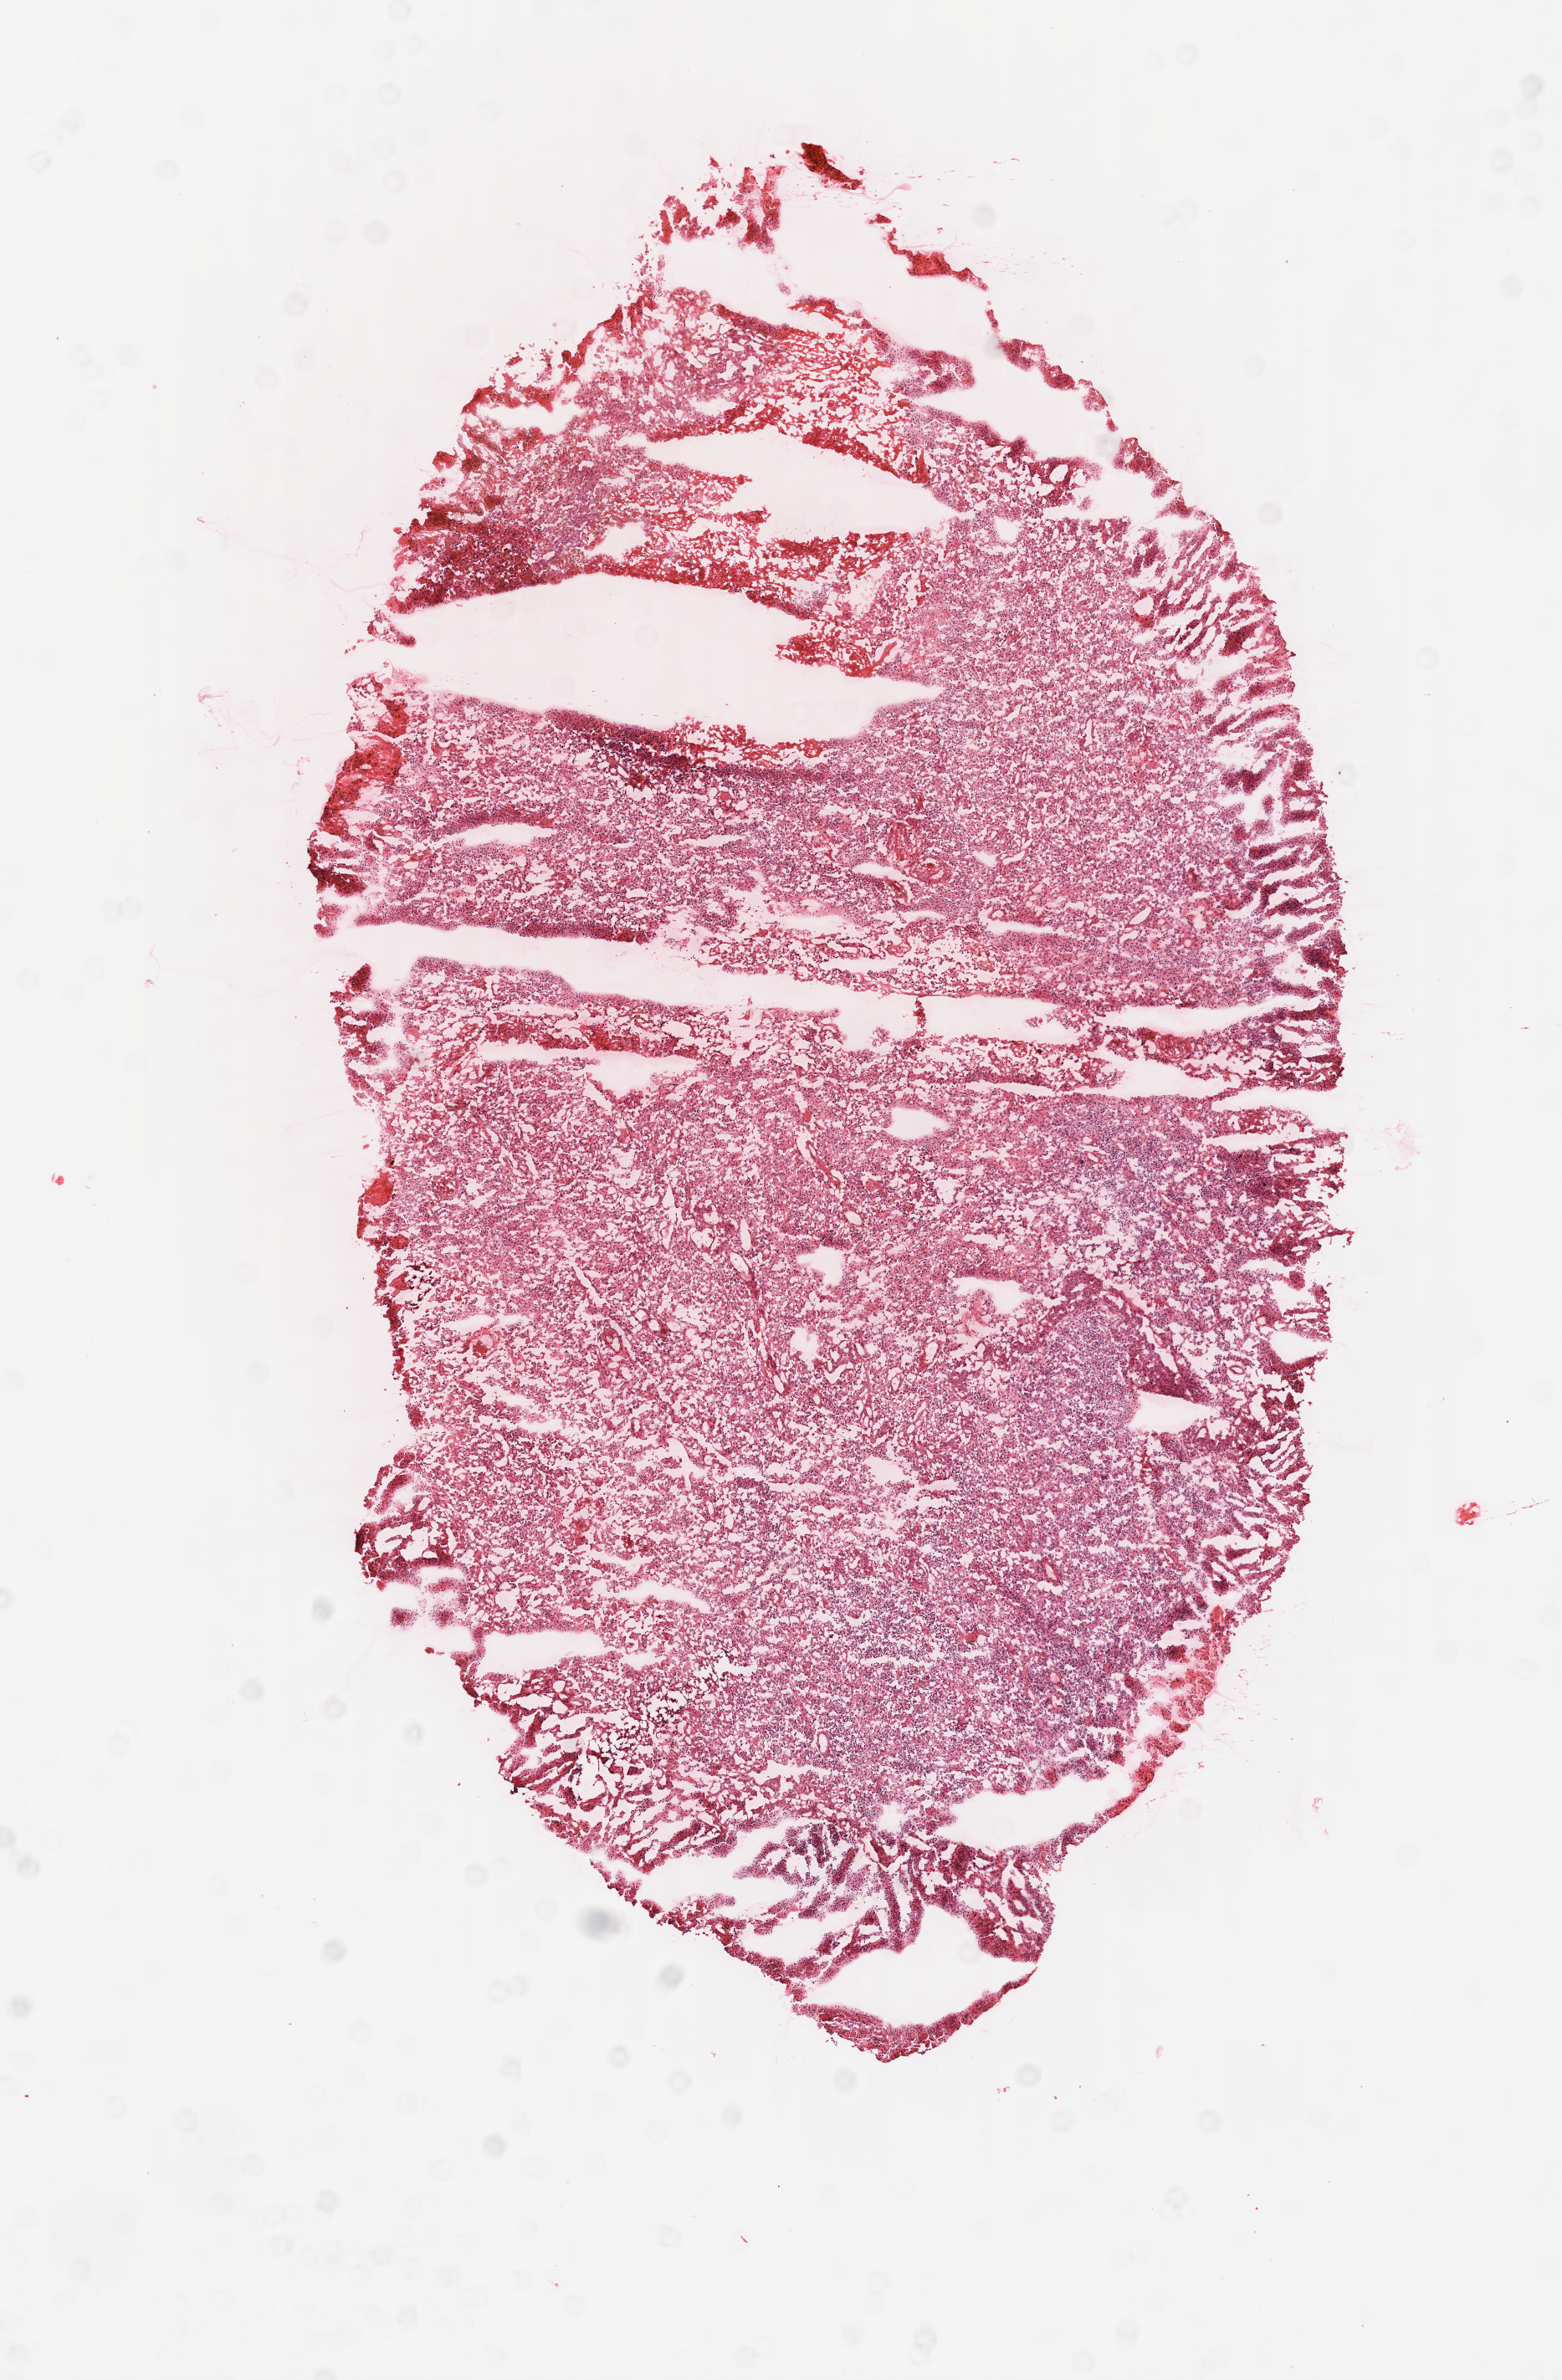
Whole-slide histology image, H&E-stained, a low-resolution overview of the entire scanned area, about 7.6 x 11.5 mm. Frozen section from the top of the tissue portion. Sample: primary tumour, brain. Male patient; age at initial diagnosis 40 years. Slide review estimates, as recorded: tumour cells 90%, tumour nuclei 100%, normal cells 0%, stromal cells 0%, necrosis 10%.
Histologic diagnosis: Glioblastoma.